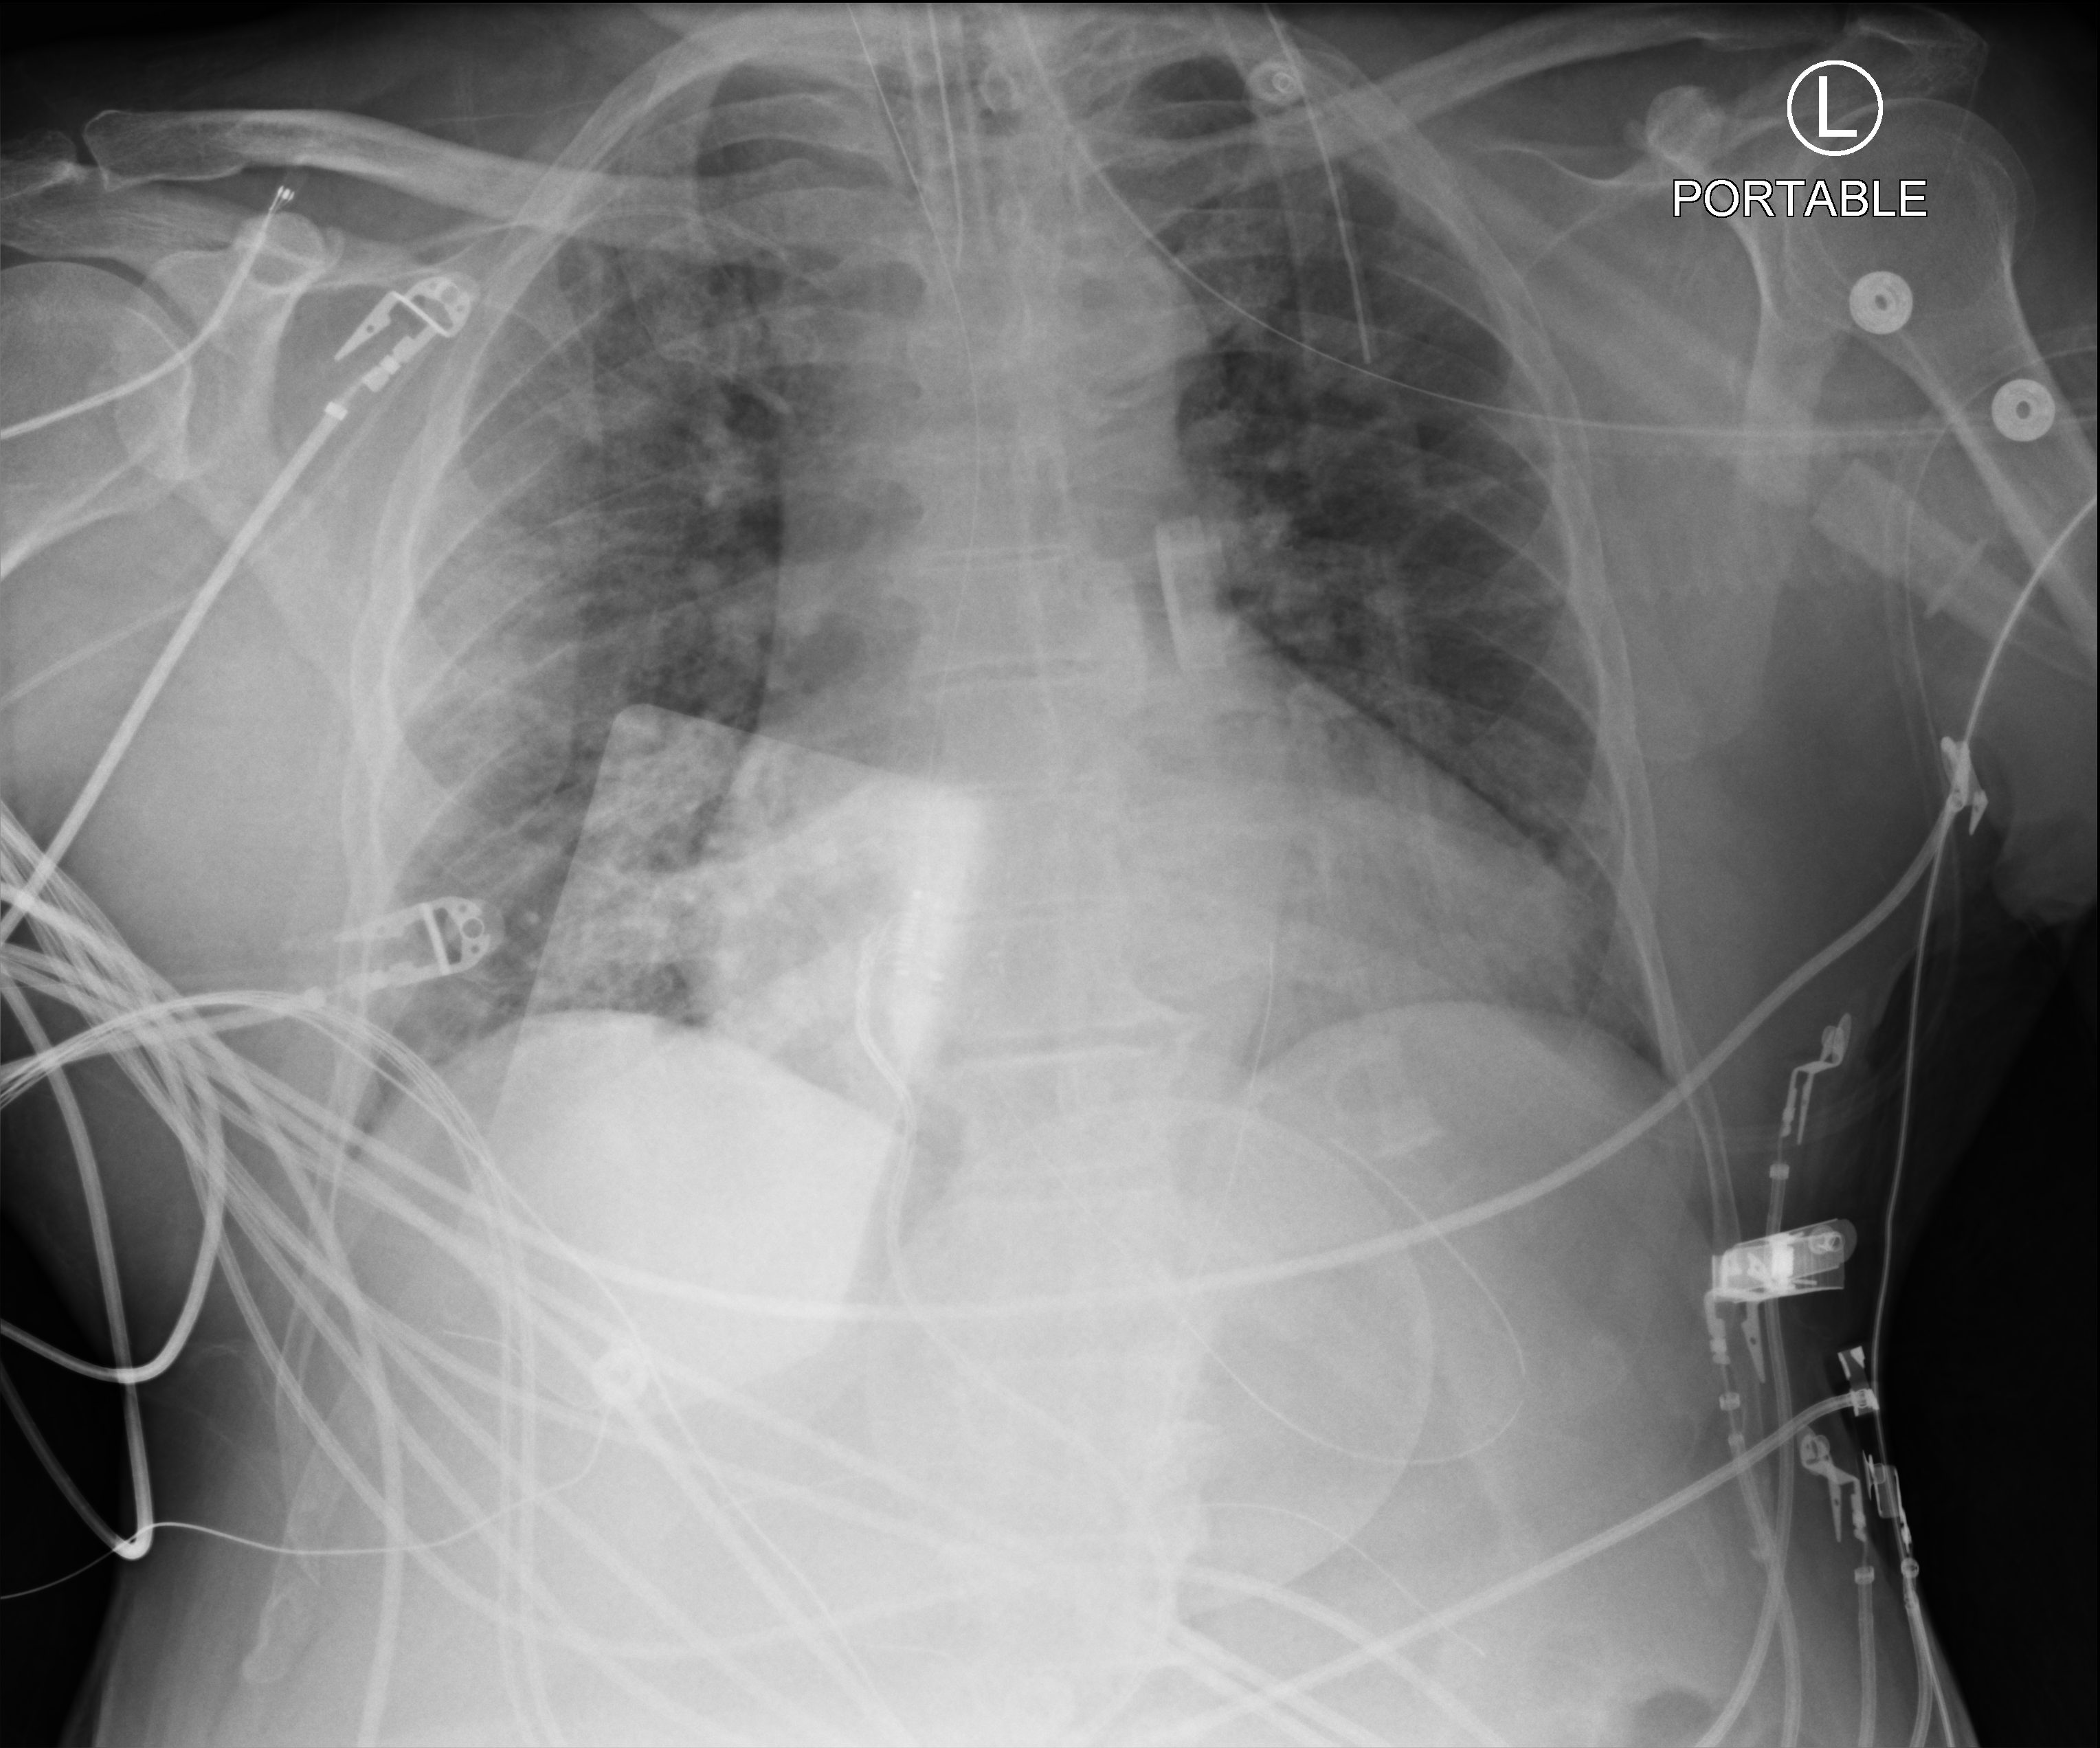
Chest X-ray (portable); anteroposterior (AP) projection. Patient hospitalised with COVID-19; male, aged 60–74 years.
Hospital-stay facts (about this admission, not read from this image; timing relative to this image not recorded):
- COPD (admission record): no